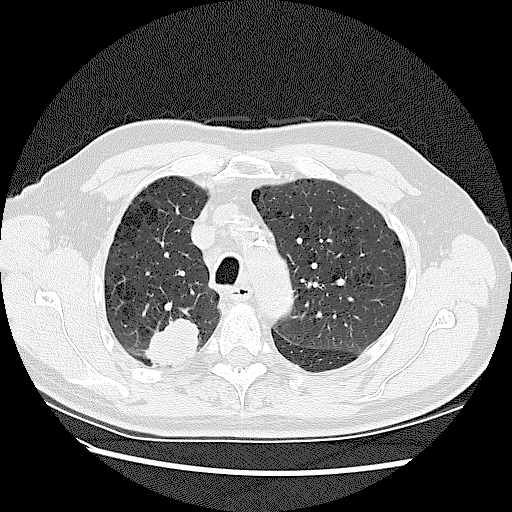
Chest CT (low-dose screening protocol), one axial image; first (baseline) screen; lung window (W 1500 / L -600 HU); 2.5 mm slice thickness; lung (sharp) reconstruction kernel (LUNG); 120 kVp; 512 × 512 image matrix. Male, age 72 years at enrolment. Current smoker at enrolment.
• Lesion marked by an expert reader, bounding box [x1, y1, x2, y2] px = [137, 310, 213, 376].
• The screening reader recorded 2 non-calcified nodules or masses ≥4 mm on this exam (right upper lobe, right upper lobe); which of them this box marks is not recorded.
• Official screen result: positive, change unspecified: nodule(s) >= 4 mm or enlarging nodule(s), mass(es), or other non-specific abnormalities suspicious for lung cancer.
• Later outcome: lung cancer diagnosed 42 days after this screen — adenocarcinoma, NOS, right upper lobe, stage IV (AJCC 6th edition), 45 mm at pathology.